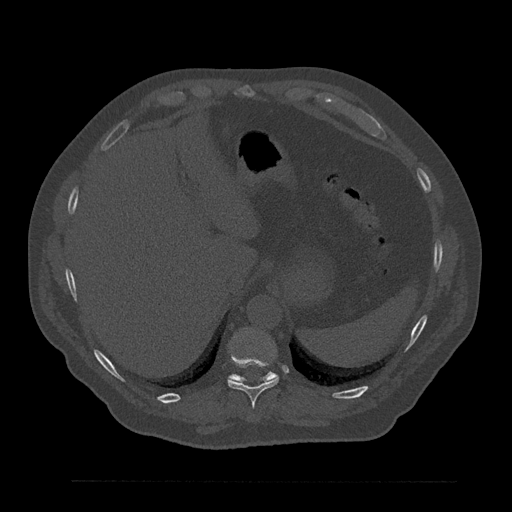
CT including the spine, one axial slice. Position 332 of 797 along the scan axis. Reconstruction kernel Br40s/3. 120 kVp. Bone window (W 1800 / L 400 HU). 512 × 512 image matrix, field of view 430 × 430 mm. Male patient, age 61 years. Case-level facts recorded for this patient, not image findings: primary cancer: prostate.
Outlined on this slice (semi-automatic segmentation, software-assisted and operator-edited):
- T10 vertebra: box from (x=227, y=351) to (x=279, y=408) px
- T11 vertebra: (x=229, y=372)–(x=277, y=382)